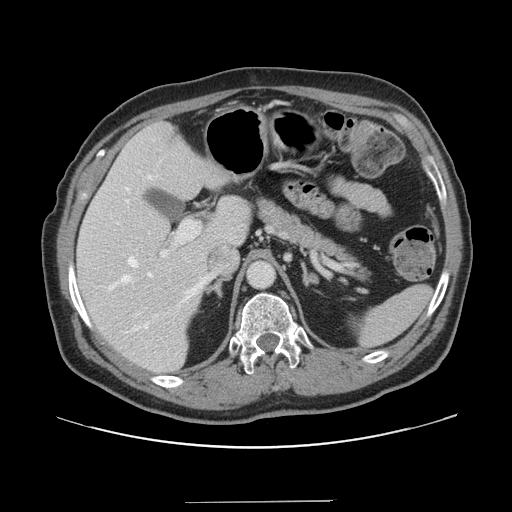
Contrast-enhanced abdominal CT, one axial slice; slice 96 of 151 in the series (ordered by position); 120 kVp; intravenous contrast given; soft-tissue window (W 400 / L 40 HU); 2.5 mm slice thickness; 512 × 512 image matrix, field of view 399 × 399 mm. Male patient, age 63 years. Case-level facts recorded for this patient, not image findings: diagnosis: colorectal cancer liver metastases, imaged before liver resection; multiple liver metastases: no; largest metastasis: 2.1 cm.
Structures marked on this image (outlined manually by an expert reader):
- hepatic veins: bounding box (x1, y1, x2, y2) in pixels: (109, 175, 213, 333)
- liver: (77, 123, 251, 373)
- planned liver remnant (the part of the liver to remain after resection): (77, 123, 249, 373)
- portal vein (with intrahepatic branches): (161, 220, 200, 257)